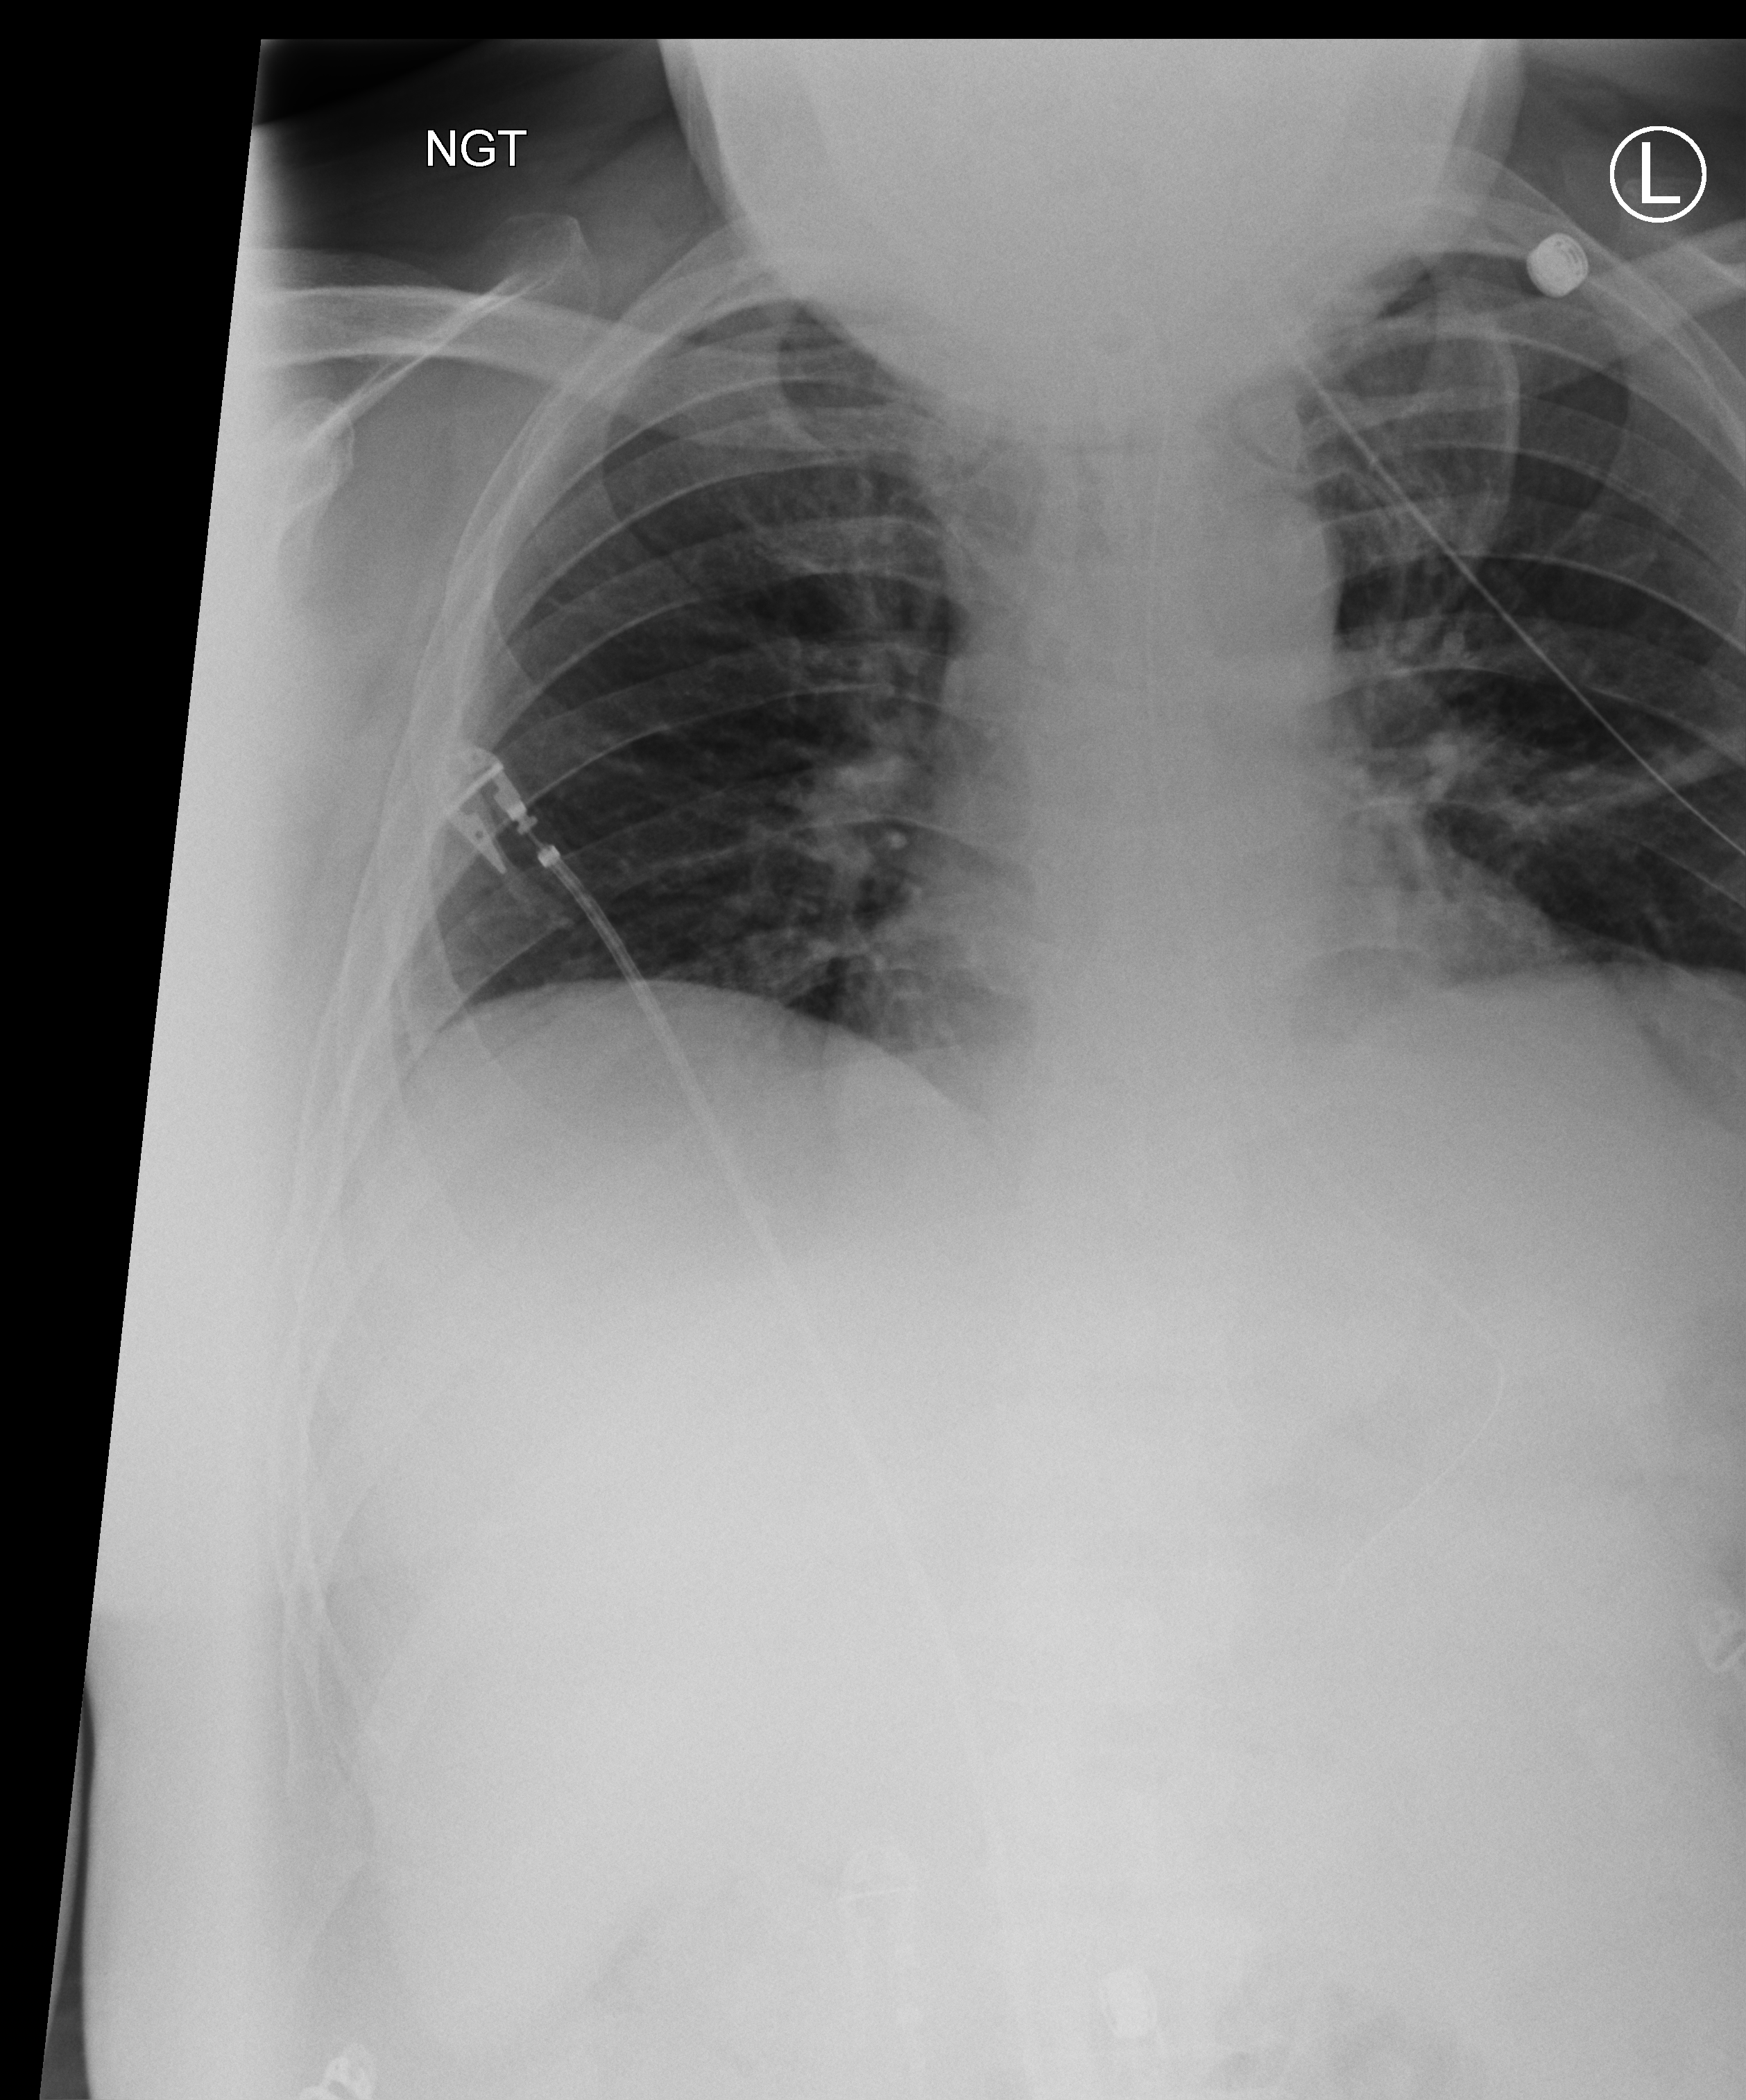
Portable chest radiograph, anteroposterior (AP) projection. Male patient hospitalised with COVID-19, age 18–59 years.
From the hospital-stay record, not from the radiograph (when in the stay this image was taken is not recorded): length of hospital stay: 65 days; admitted to intensive care during this hospital stay: yes.